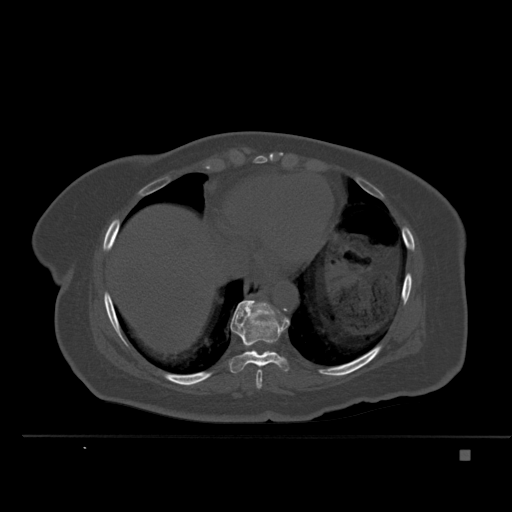
CT including the spine, one axial slice. Position 297 of 477 along the scan axis. Bone window (W 1800 / L 400 HU). 512 × 512 image matrix, field of view 422 × 422 mm. Patient: female, 74 years. Case-level facts recorded for this patient, not image findings: primary cancer: colon.
Structures marked on this image (semi-automatically segmented with operator editing):
- T10 vertebra: bounding box (x1, y1, x2, y2) in pixels: (241, 301, 280, 352)
- T8 vertebra: (256, 369, 263, 389)
- T9 vertebra: (229, 300, 290, 373)